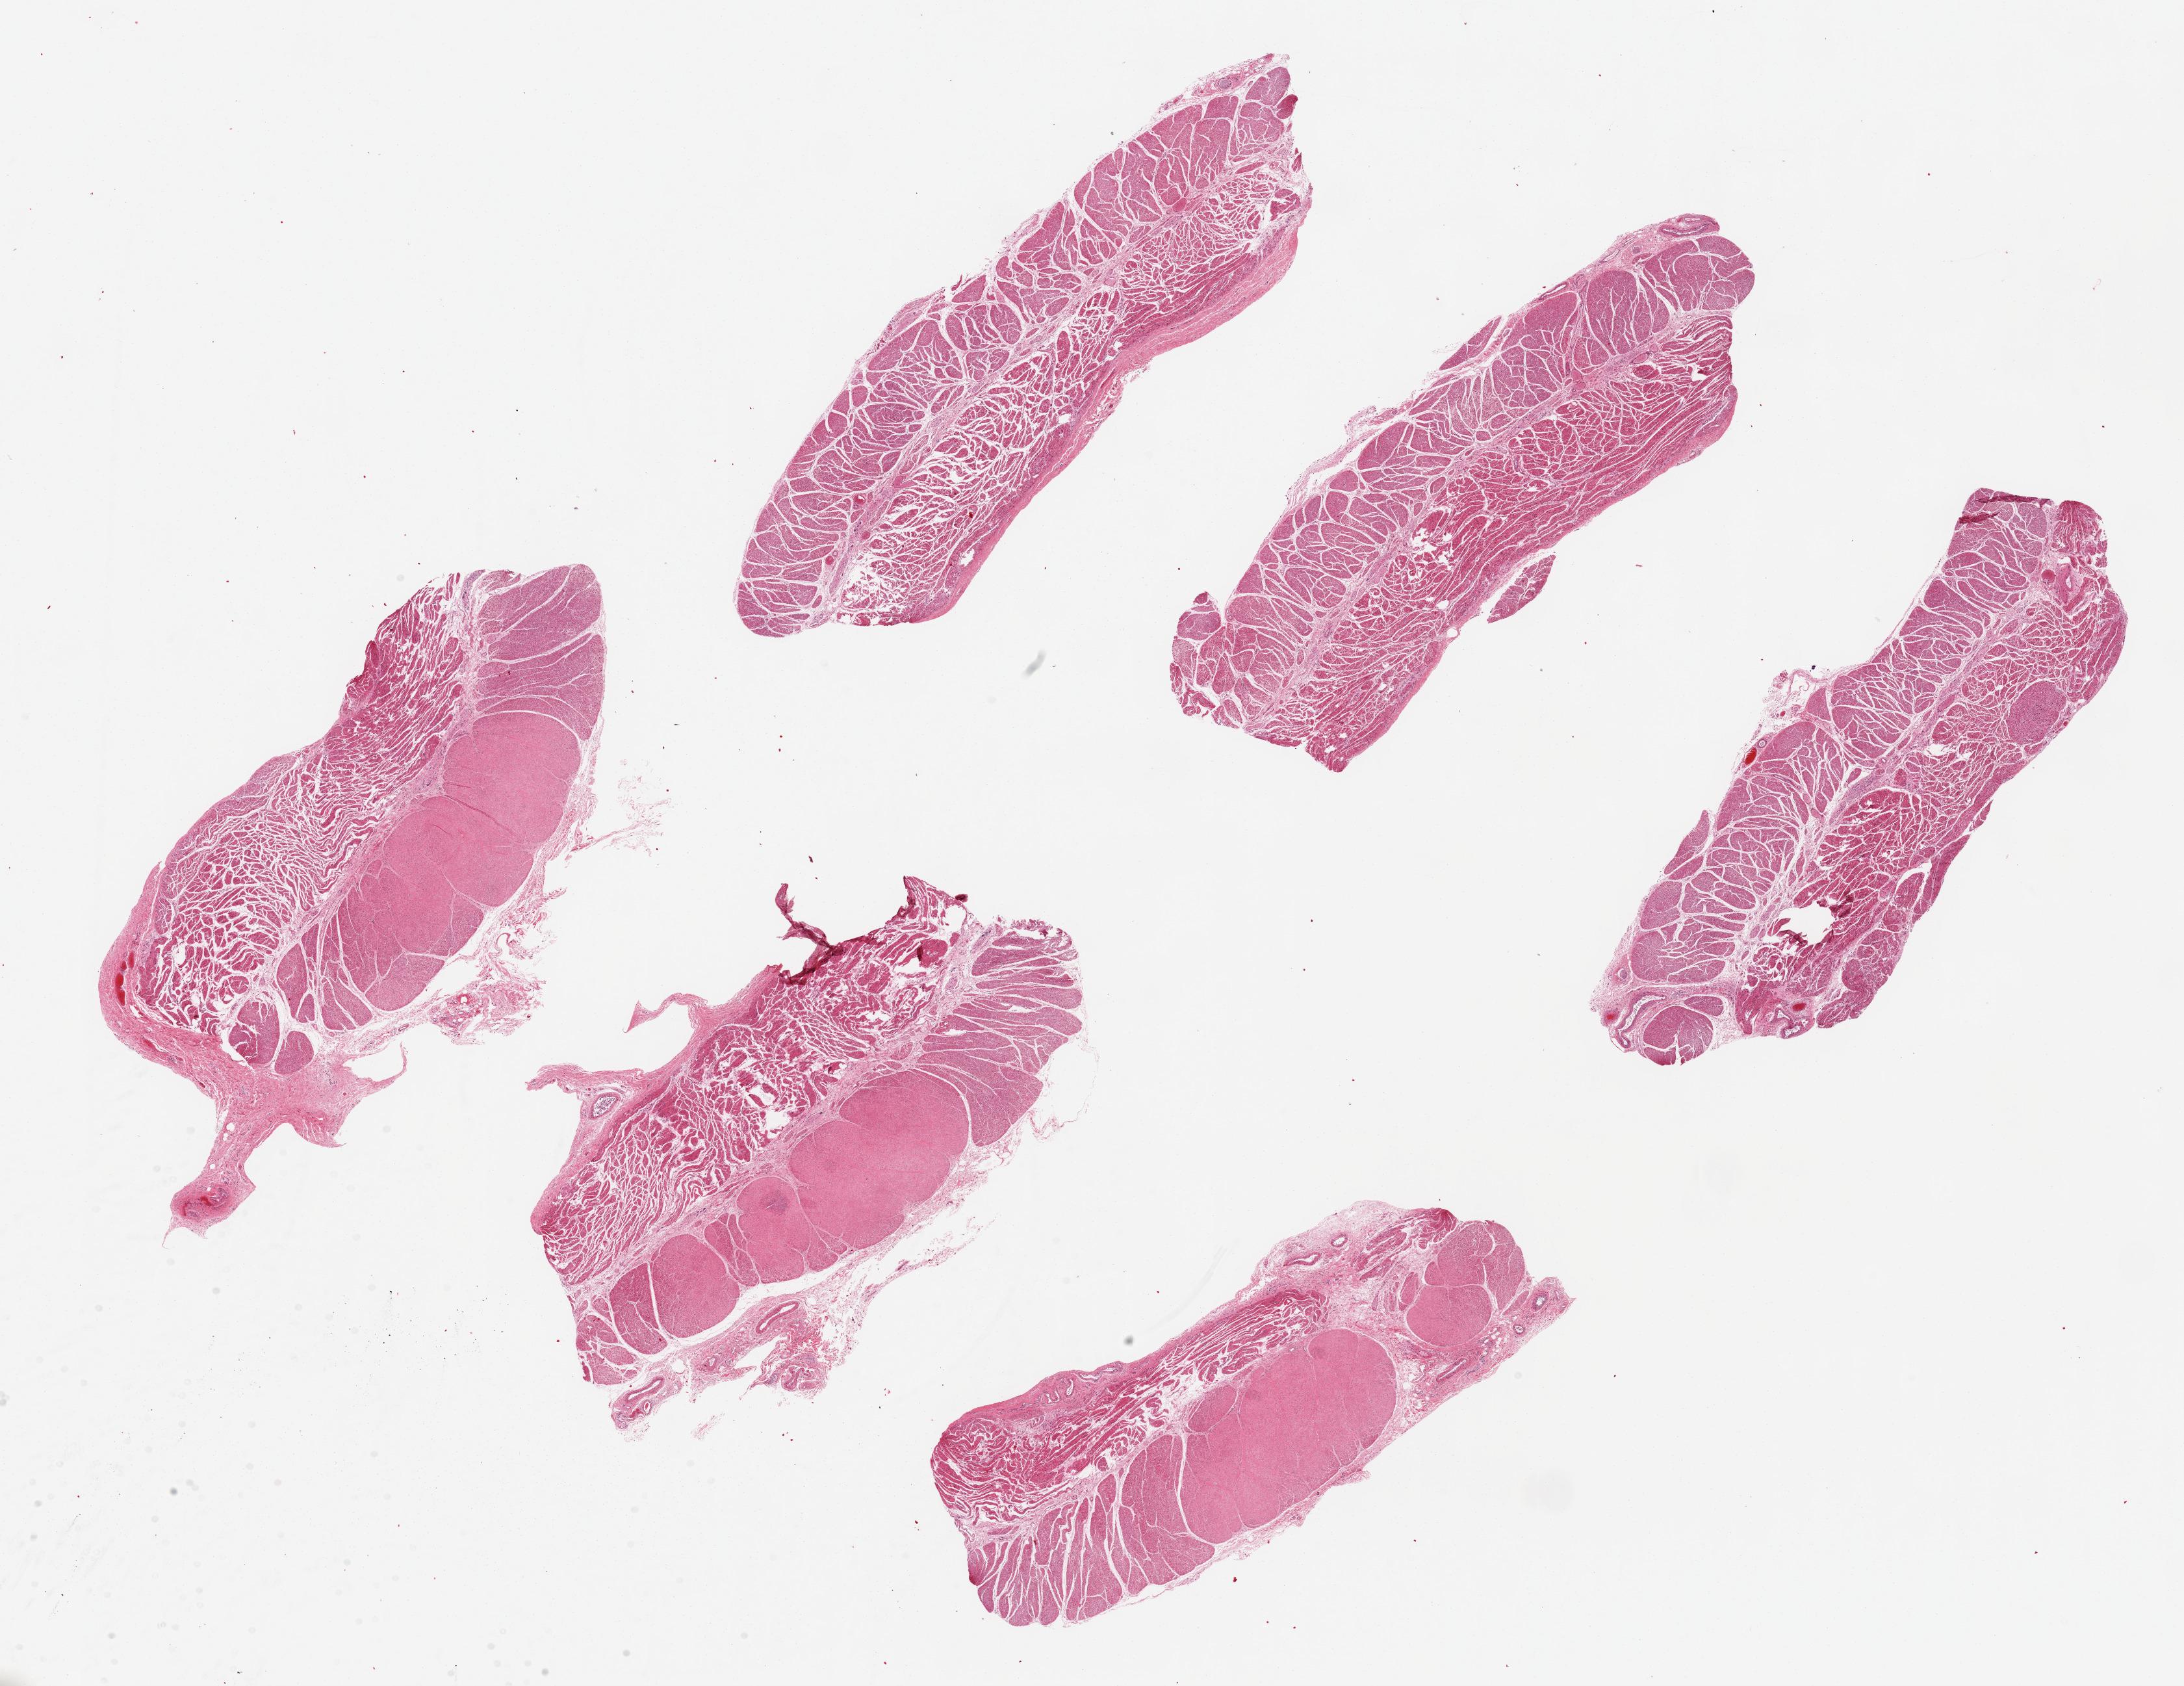
Whole-slide image, H&E stain, low-resolution overview of the scanned area, about 26.6 x 20.5 mm (acquisition: 20x scan); PAXgene-fixed, paraffin-embedded tissue; section of esophageal muscle (target tissue); tissue donor sample. Donor: male.
* review note (as recorded): 6 pieces ~ 8x2.5mm